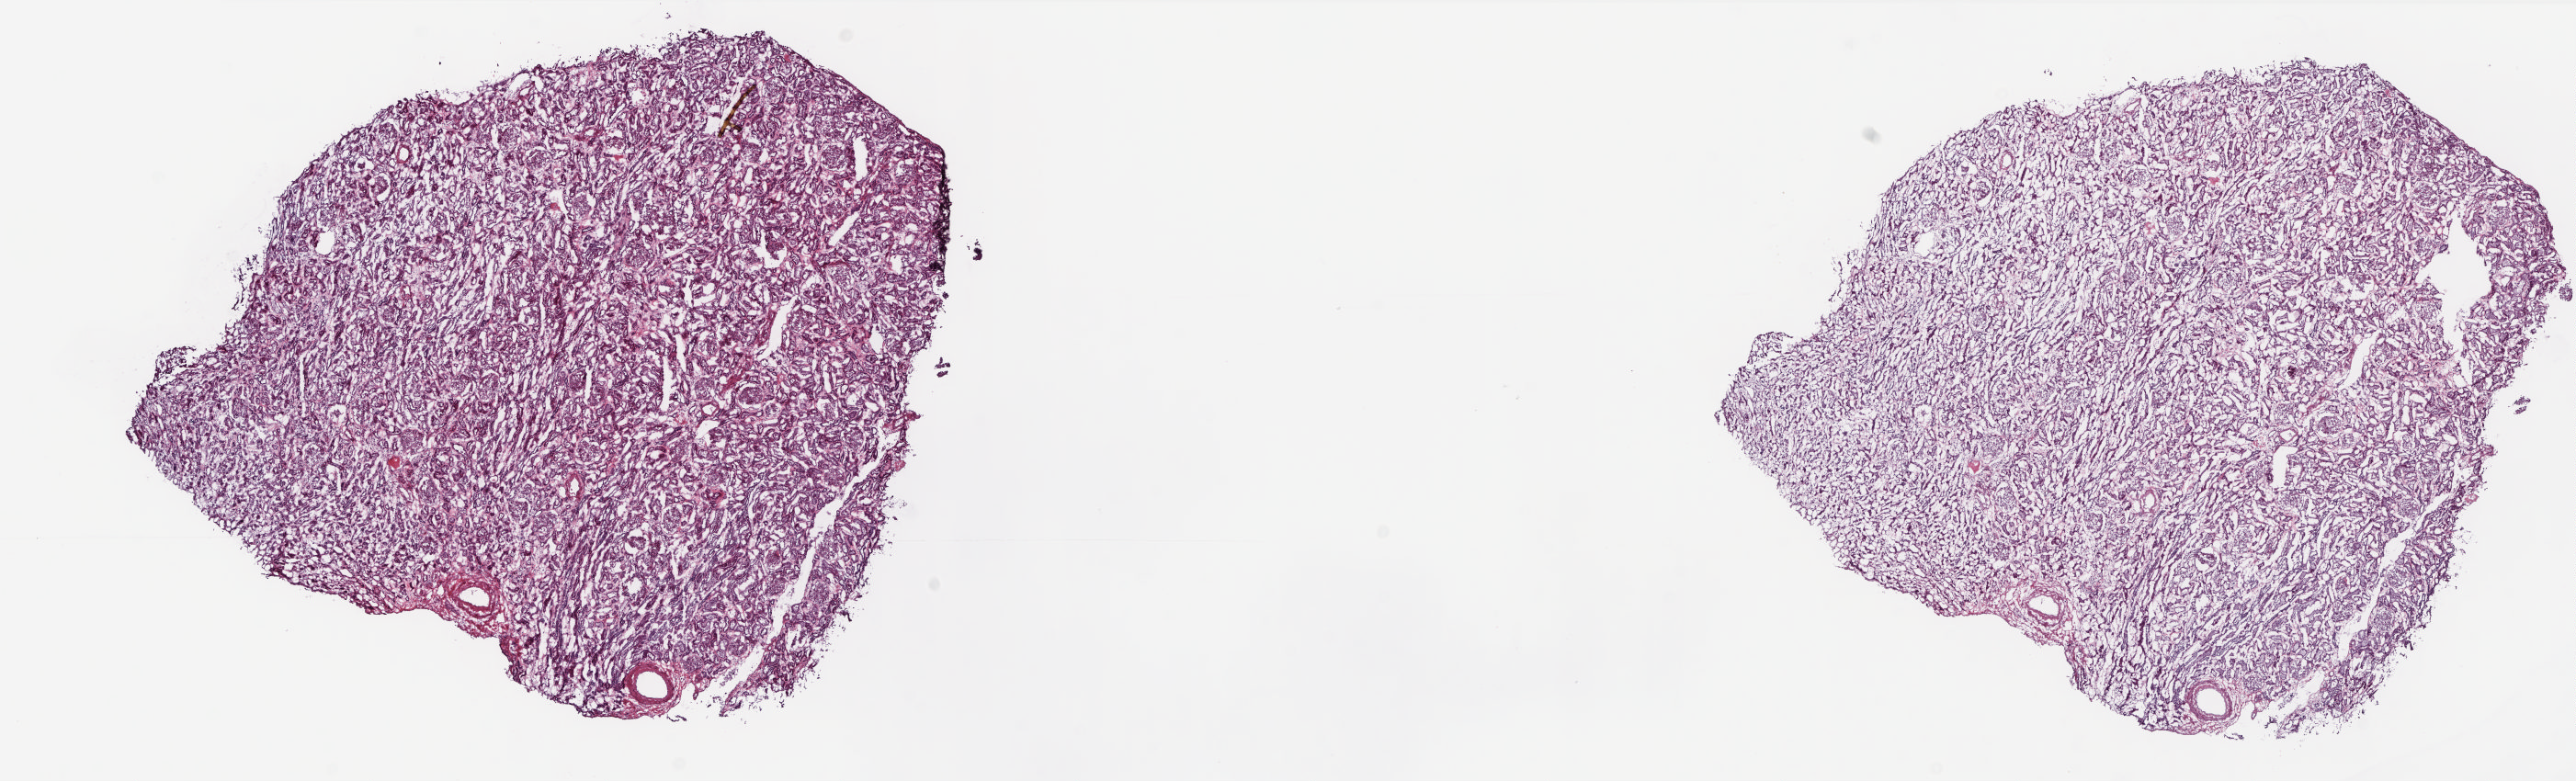
Whole-slide histology image, H&E, shown as a low-resolution overview of the whole scanned area (about 22.6 x 6.9 mm). Frozen section from the top of the tissue portion. Solid tissue normal (non-tumour tissue) sample from the kidney. Female patient; age at initial diagnosis 61 years. Pathologist review of this section (percent, as recorded): tumour cells 0%, tumour nuclei 0%, normal cells 100%, stromal cells 0%, necrosis 0%. Infiltration values recorded for this section: lymphocyte infiltration 1%, monocyte infiltration 2%, neutrophil infiltration 0%.
- this section: solid tissue normal (non-tumour) sample from the same patient
- patient diagnosis: Papillary adenocarcinoma, NOS